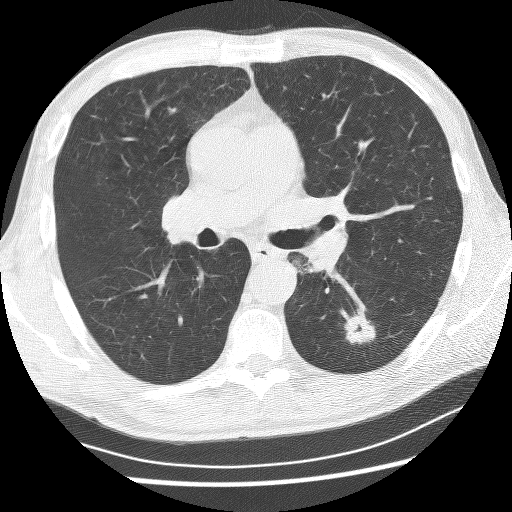
Chest CT (low-dose screening protocol), one axial image. Baseline annual screen. Lung window (W 1500 / L -600 HU). 512 × 512 image matrix, field of view 340 × 340 mm. Male participant, aged 62 years at enrolment. Current smoker at enrolment.
- Expert-annotated lung lesion, bounding box [x1, y1, x2, y2] px = [330, 307, 383, 352].
- Reader record for this screening exam (exam-level; its link to the box is not recorded): non-calcified nodule or mass ≥4 mm, left lower lobe, 21 × 17 mm, spiculated (stellate) margins, soft tissue attenuation.
- Official screen result: positive, change unspecified: nodule(s) >= 4 mm or enlarging nodule(s), mass(es), or other non-specific abnormalities suspicious for lung cancer.
- Later outcome: lung cancer diagnosed 58 days after this screen — non-small cell carcinoma, left lower lobe, poorly differentiated (G3), stage IA (AJCC 6th edition), 11 mm at pathology.